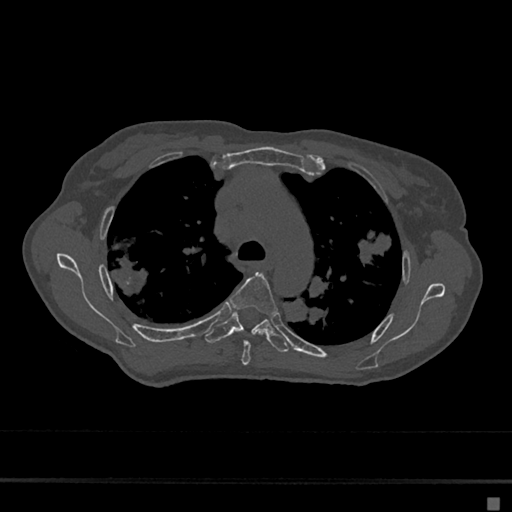
CT including the spine, one axial slice. Position 483 of 797 along the scan axis. Reconstruction kernel Br40s/3. Bone window (W 1800 / L 400 HU). 0.5 mm slice thickness. 512 × 512 image matrix, field of view 360 × 360 mm. Patient: female, 68 years. Case-level facts recorded for this patient, not image findings: primary cancer: renal.
Outlined on this slice (semi-automatically segmented with operator editing):
- T4 vertebra: bounding box [x1, y1, x2, y2] px = [228, 272, 278, 366]
- T5 vertebra: [205, 310, 289, 353]